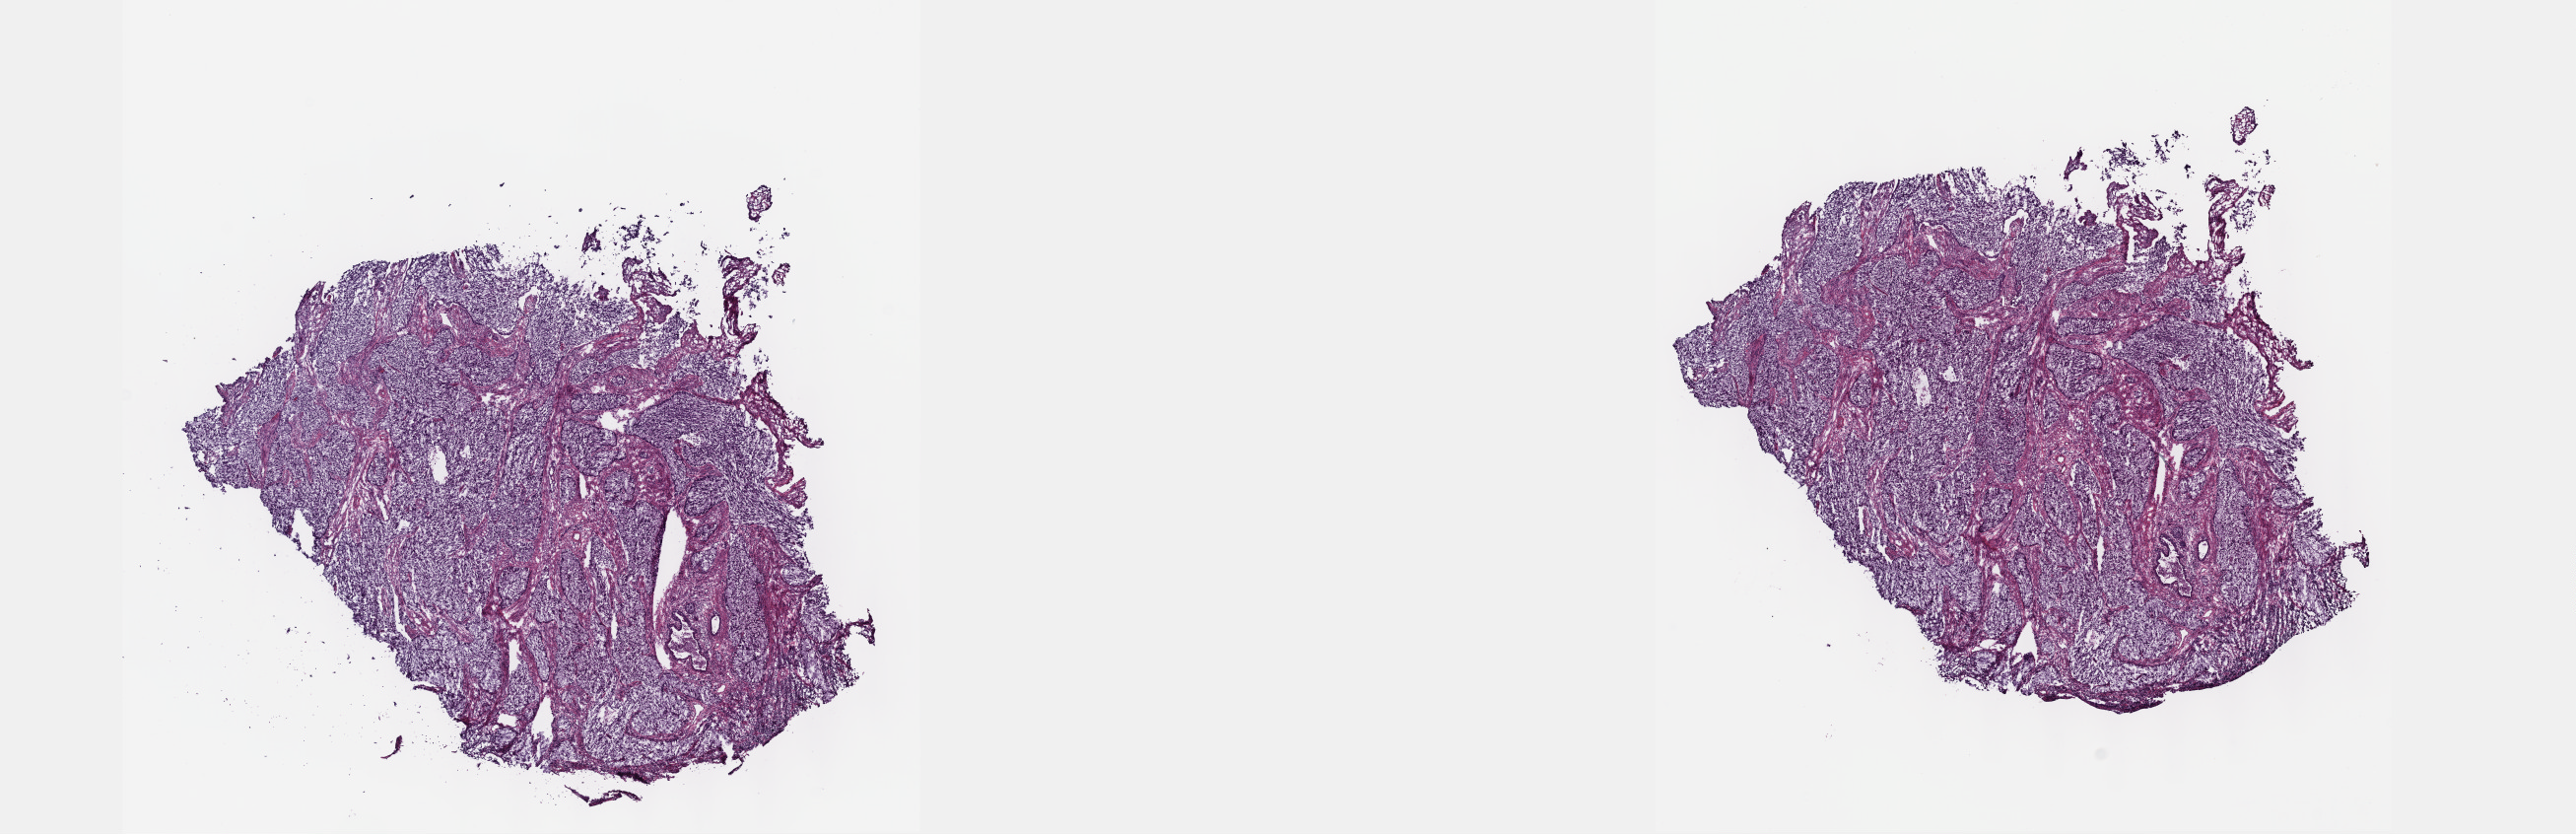
H&E whole-slide image — shown as a low-resolution overview of the whole scanned area (about 21.1 x 6.8 mm, acquisition: 40x scan). Frozen section from the top of the tissue portion. Cervix, primary tumour sample. Patient: female, age at initial diagnosis 35 years.
Diagnosis: Mucinous adenocarcinoma, endocervical type (cervix uteri).